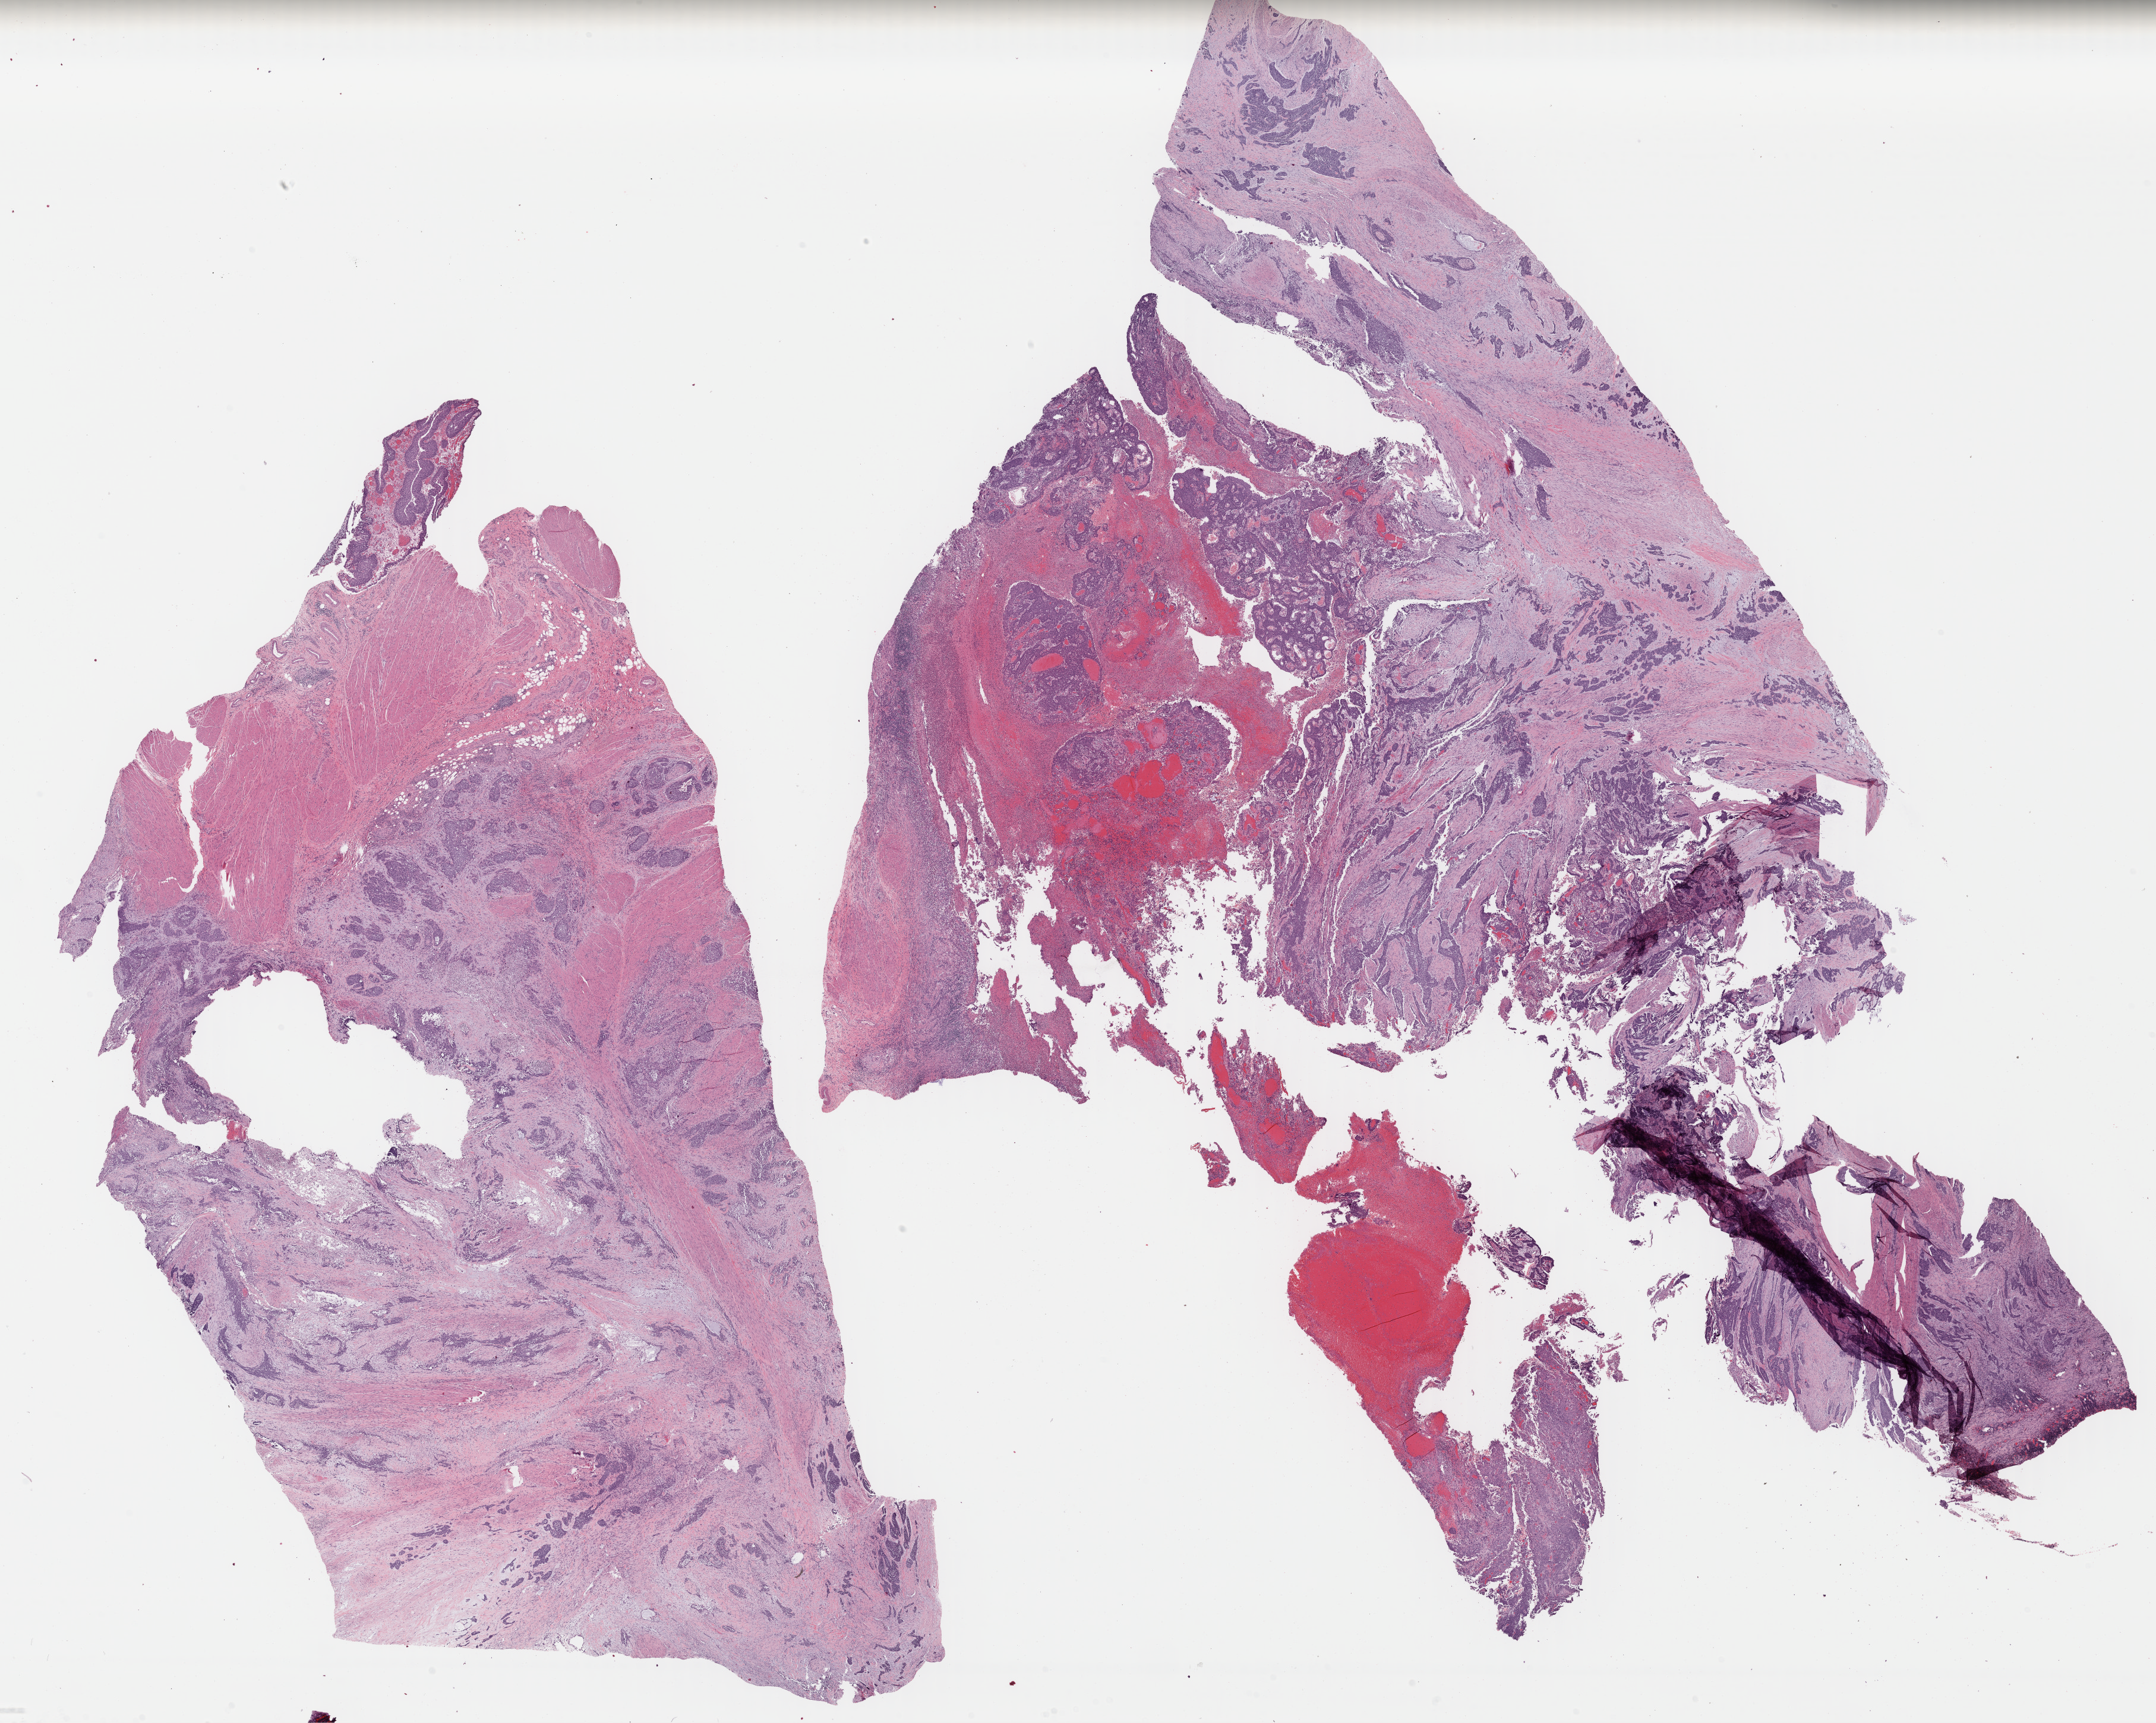
Whole-slide histology image, H&E-stained — low-resolution overview of the scanned area, about 28.5 x 22.8 mm, formalin-fixed paraffin-embedded (FFPE) diagnostic section, primary tumour sample from the bladder. Male, age 59 years at initial diagnosis. Histologic grade: high grade.
Lymph nodes positive (case pathology): 1 of 14 examined. Pathologic diagnosis: Papillary transitional cell carcinoma. AJCC pathologic stage: IV.